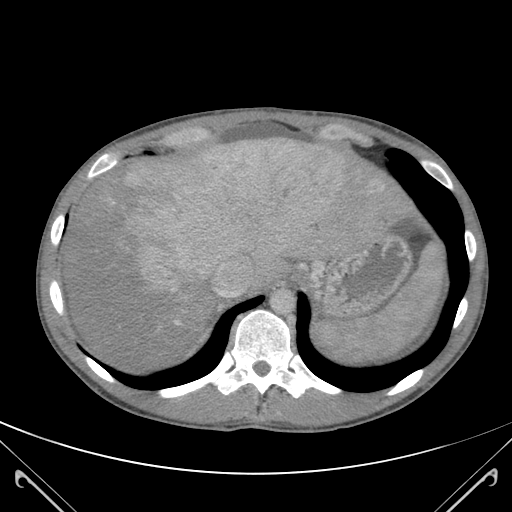
Contrast-enhanced abdominal CT (liver protocol), one axial slice. Position 97 of 118 along the scan axis. Soft-tissue window (W 400 / L 40 HU). 3 mm slice thickness. 512 × 512 image matrix, field of view 380 × 380 mm. Case-level facts recorded for this patient, not image findings: diagnosis: hepatocellular carcinoma (patient treated with transarterial chemoembolisation; whether this scan precedes or follows treatment is not stated here); TNM stage (as recorded): Stage-IIIB; Child-Pugh class: A.
Structures marked on this image (semi-automatically segmented with operator editing):
- abdominal aorta: bounding box <273,289,295,312> (left, top, right, bottom; pixels)
- liver parenchyma outside the tumour (the mass and vessels are separate outlines, so this box may not span the whole liver): <67,140,380,366>
- mass: <98,140,352,298>
- liver vessels: <174,150,340,325>